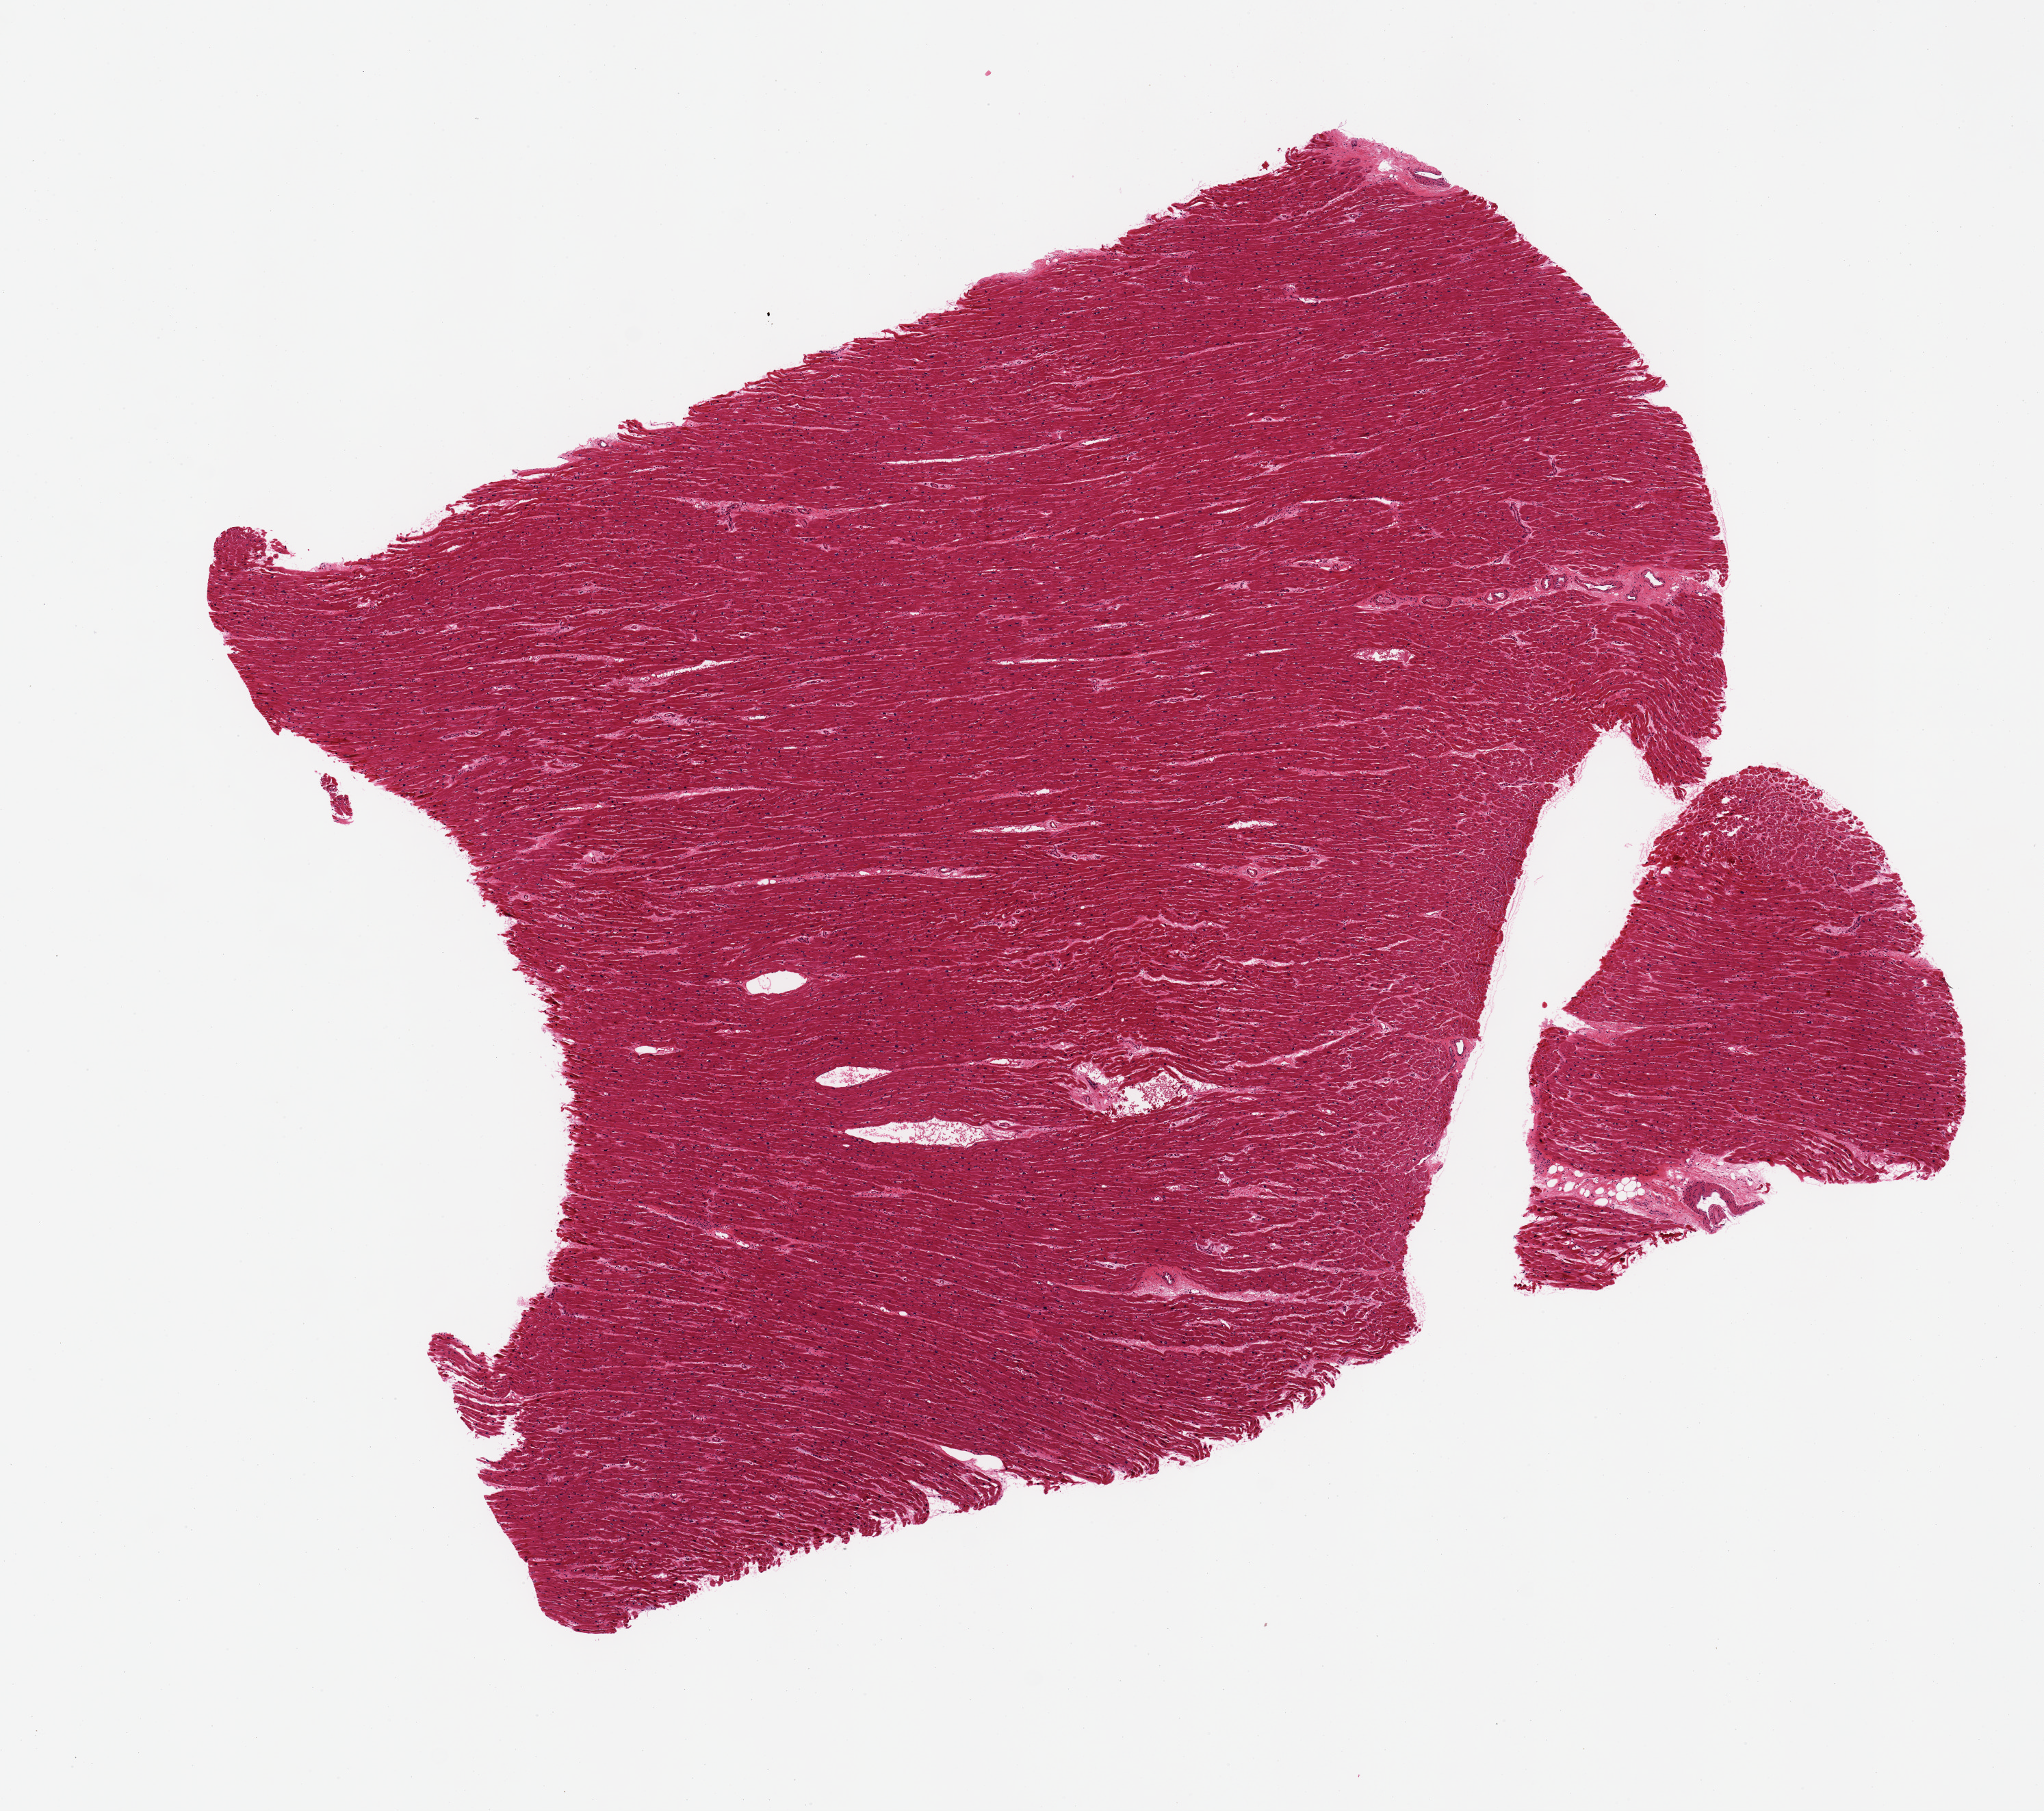
Whole-slide image, haematoxylin and eosin stain — a low-resolution overview of the entire scanned area, about 11.8 x 10.5 mm, PAXgene-fixed, paraffin-embedded tissue, section of heart (target tissue), tissue donor sample.
- review note (as recorded): Moderate ischemic changes: contraction band necrosis, nuclear hypertrophy